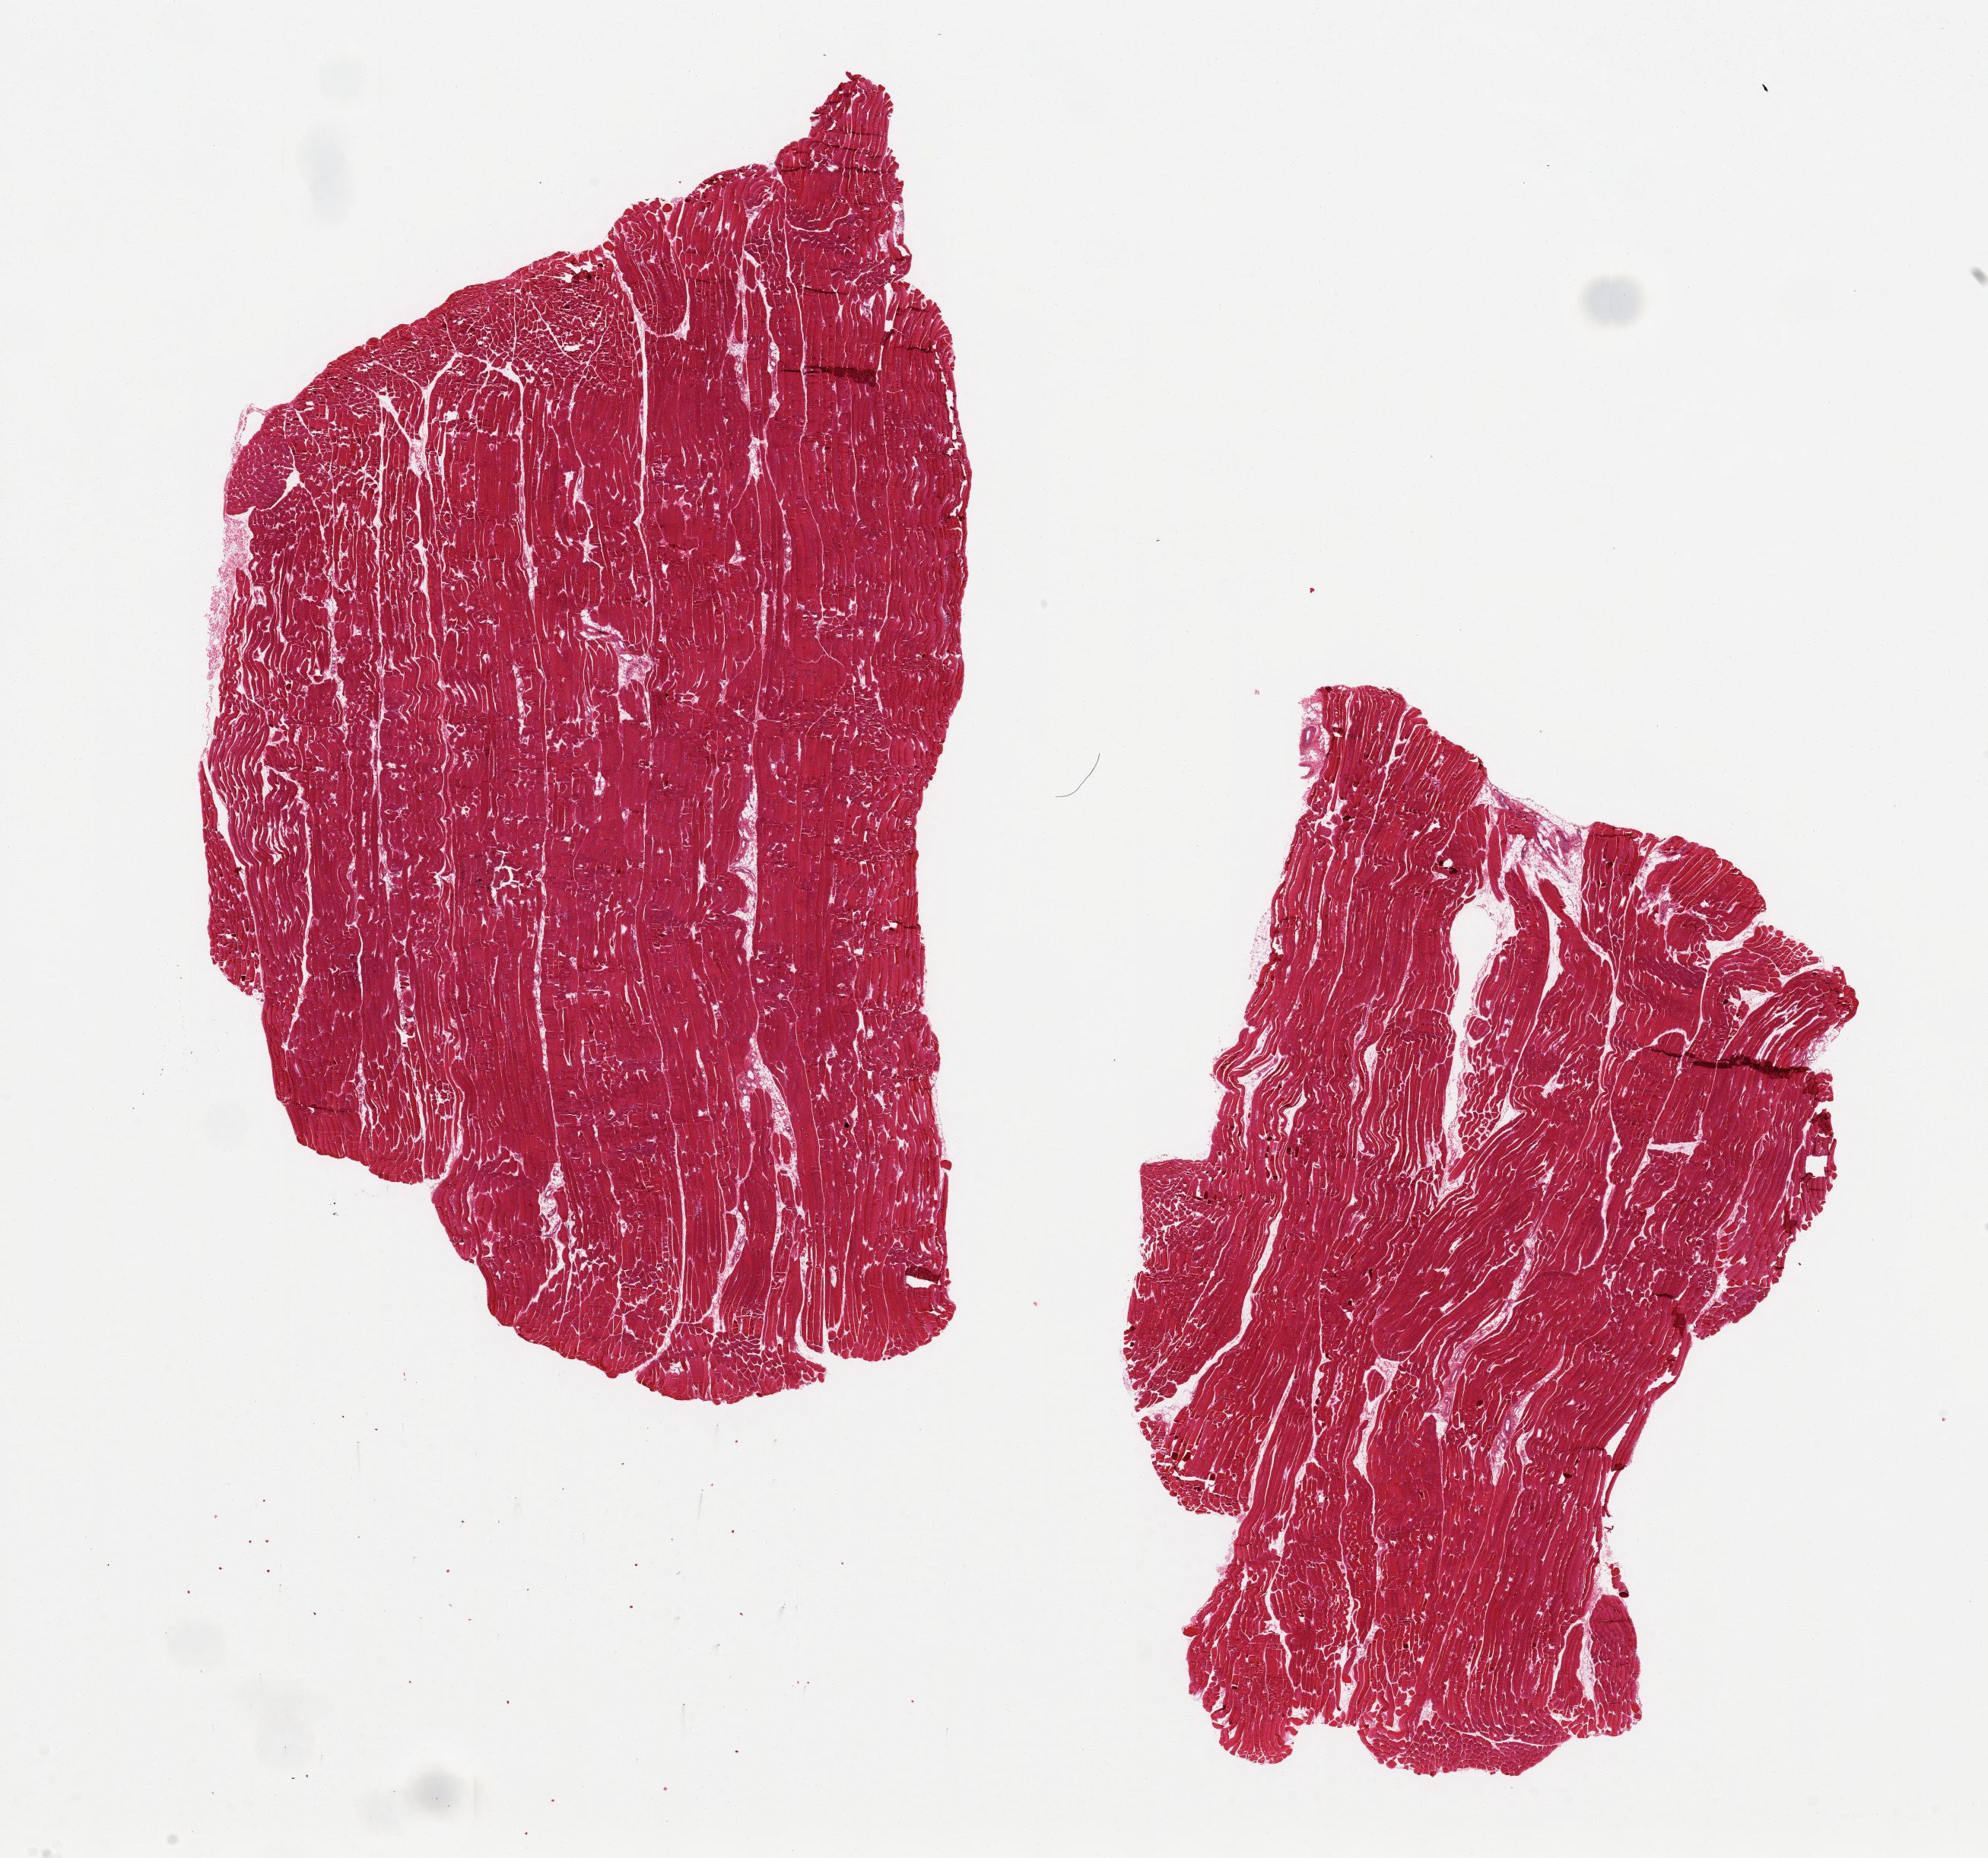
Hematoxylin and eosin (H&E) whole-slide image — low-resolution overview of the scanned area, about 20.7 x 19.3 mm (acquisition: 20x scan), PAXgene-fixed, paraffin-embedded tissue, target tissue: skeletal muscle, donor tissue sample. Male donor.
Reviewer comment on this tissue sample: 2 aliquots, 11x7mm. Minimal interstitial fat.